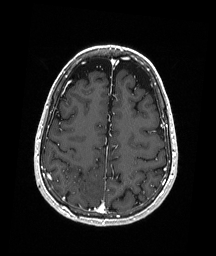
Brain MRI from a brain-tumour surgery series, one axial slice; position 68 of 192 along the scan axis; T1-weighted post-contrast; 1 mm slice thickness; 216 × 256 image matrix. Case-level facts recorded for this patient, not image findings: histopathology: Astrocytoma; WHO grade: 3; IDH mutation: yes; tumour location: Right Parietal.
Outlined on this slice (outlined manually by an expert reader):
- previous resection cavity: bounding box [x1, y1, x2, y2] px = [79, 173, 82, 177]